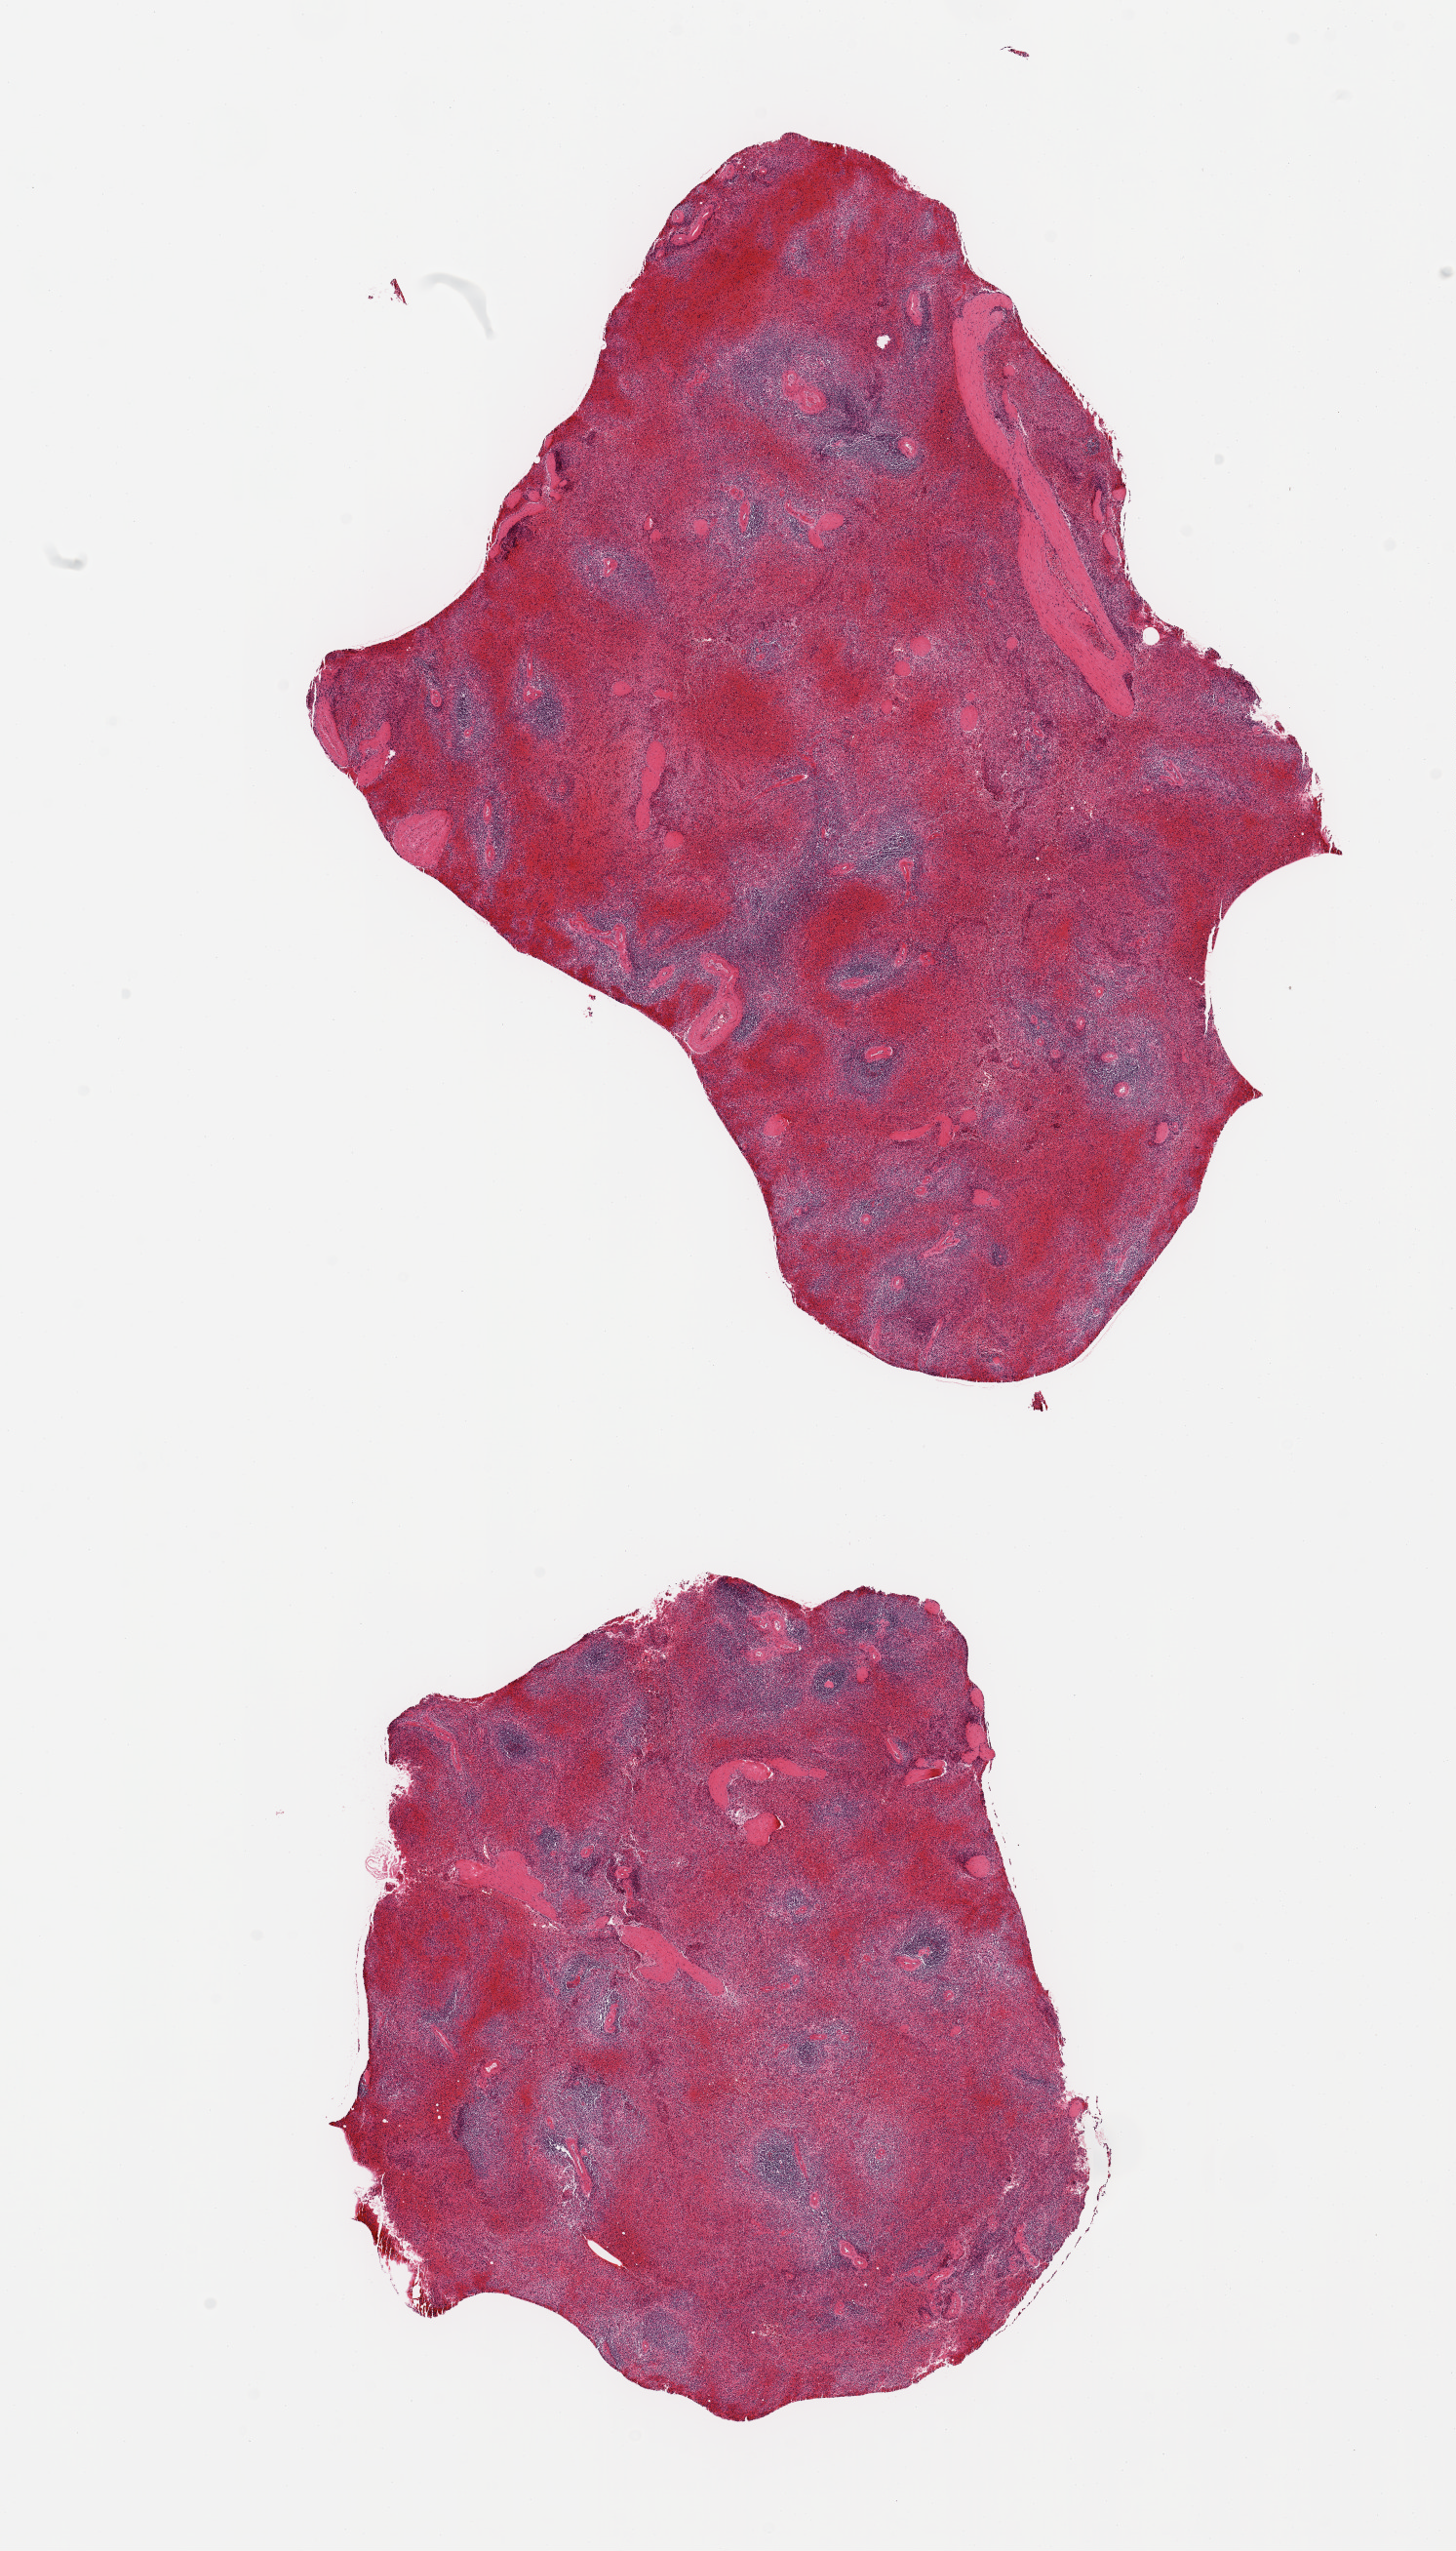
Whole-slide image, hematoxylin and eosin (H&E) stain — shown as a low-resolution overview of the whole scanned area (about 11.8 x 20.7 mm), PAXgene-fixed, paraffin-embedded tissue, sampled site (target tissue): spleen, donor tissue sample.
Pathologist's review note for this sample: 2 pieces; congested.